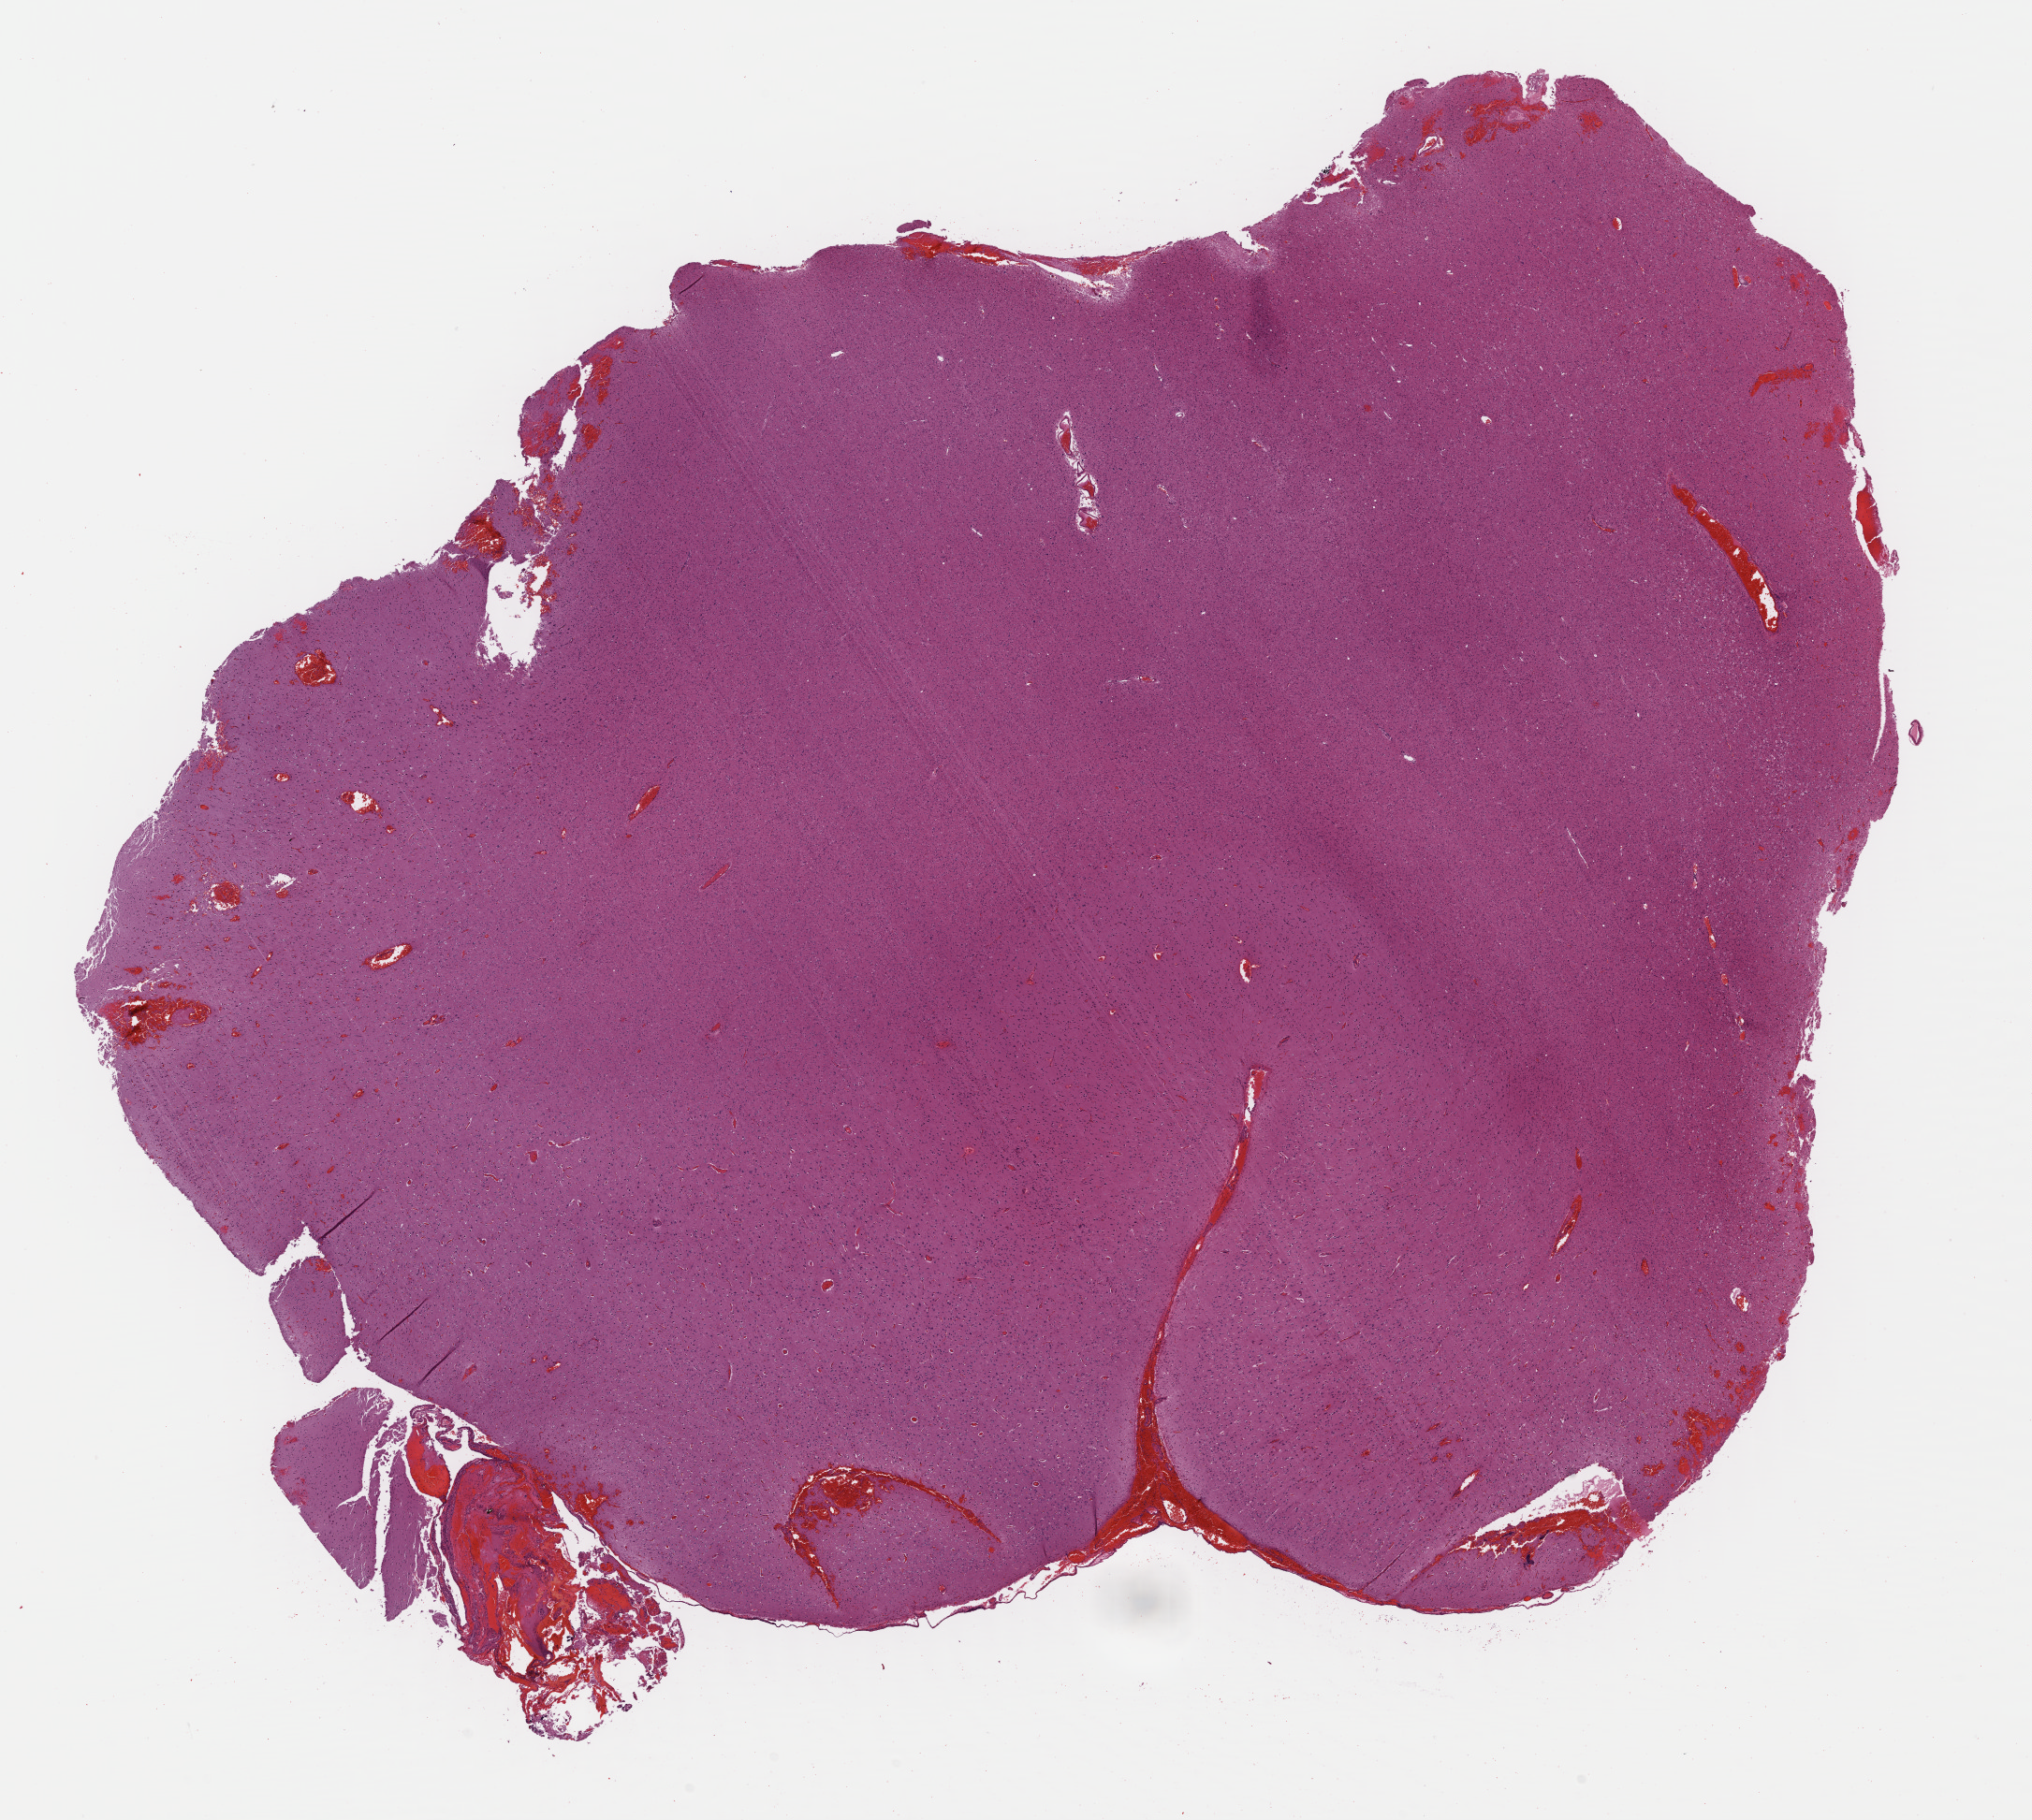
Whole-slide histology image, H&E-stained — low-resolution overview of the scanned area, about 17.1 x 15.3 mm; FFPE section; sample: primary tumour, brain. Female, age 61 years at initial diagnosis. Histologic grade: G2 (moderately differentiated).
• diagnosis: Astrocytoma, NOS (cerebrum)